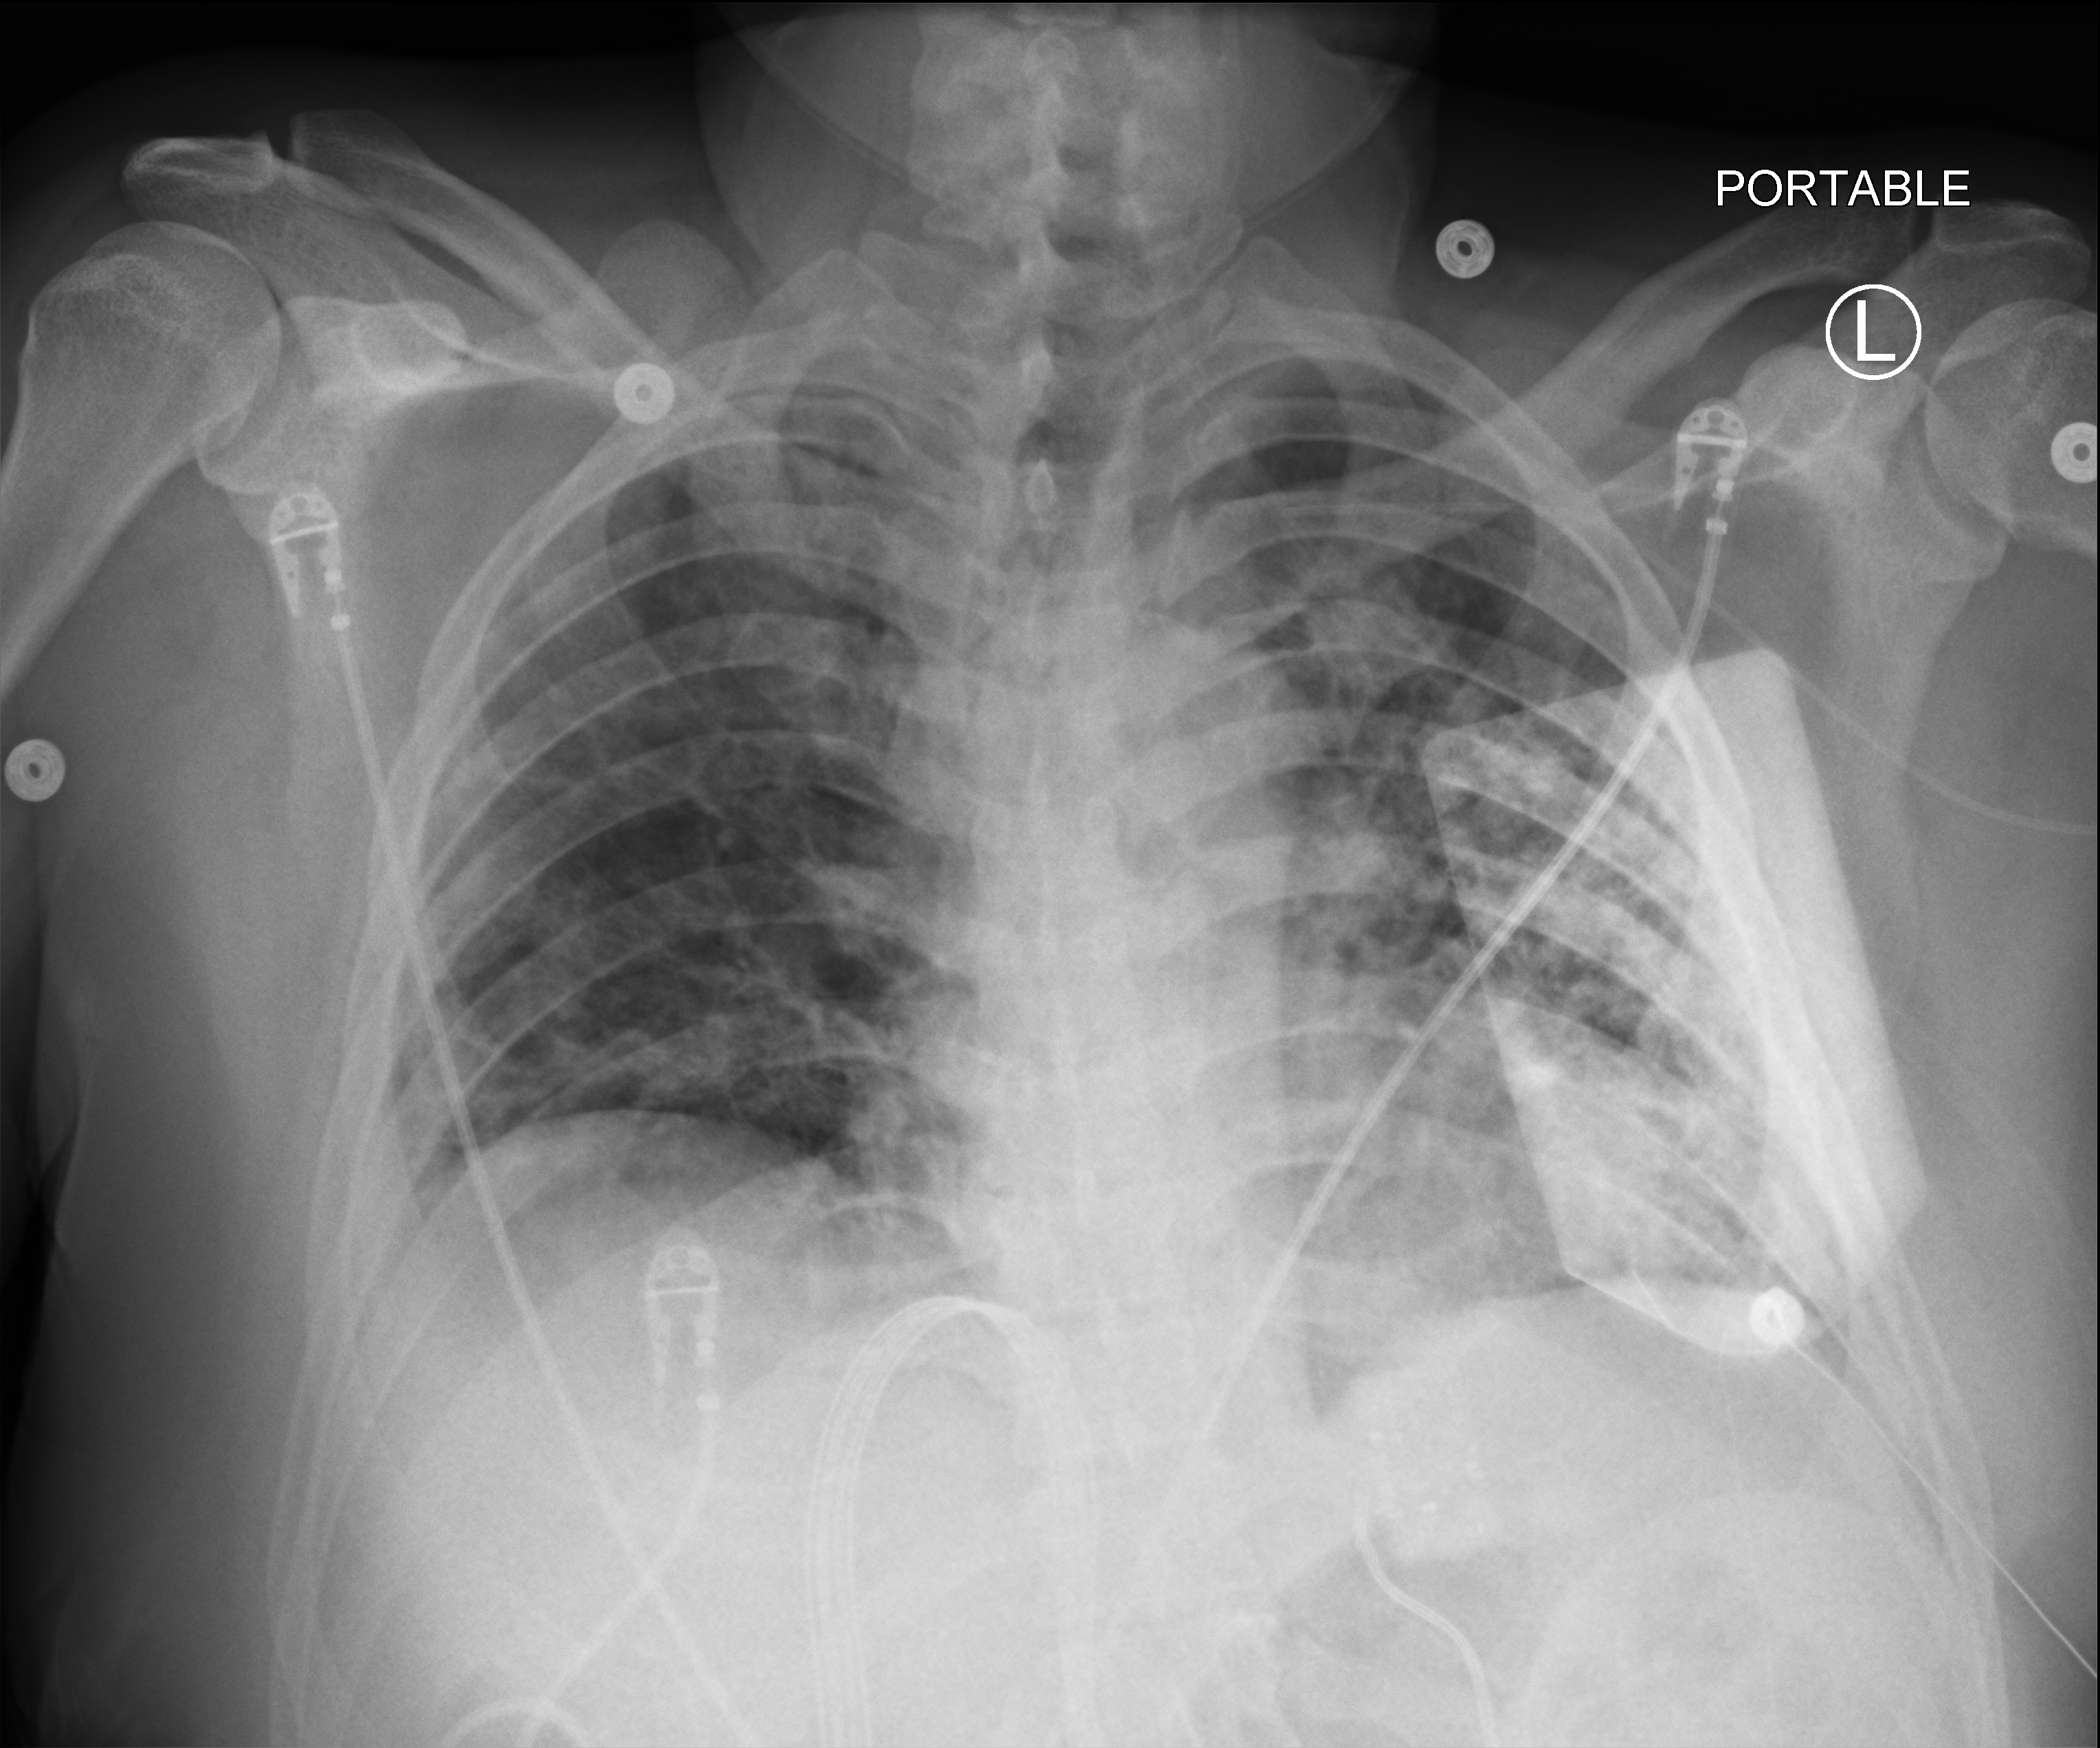
Portable chest radiograph, anteroposterior (AP) projection. Patient hospitalised with COVID-19; male, aged 18–59 years.
Admission-level facts for this patient (not findings on this image; timing relative to this image not recorded):
- length of hospital stay: 29 days
- mechanically ventilated during this hospital stay: yes